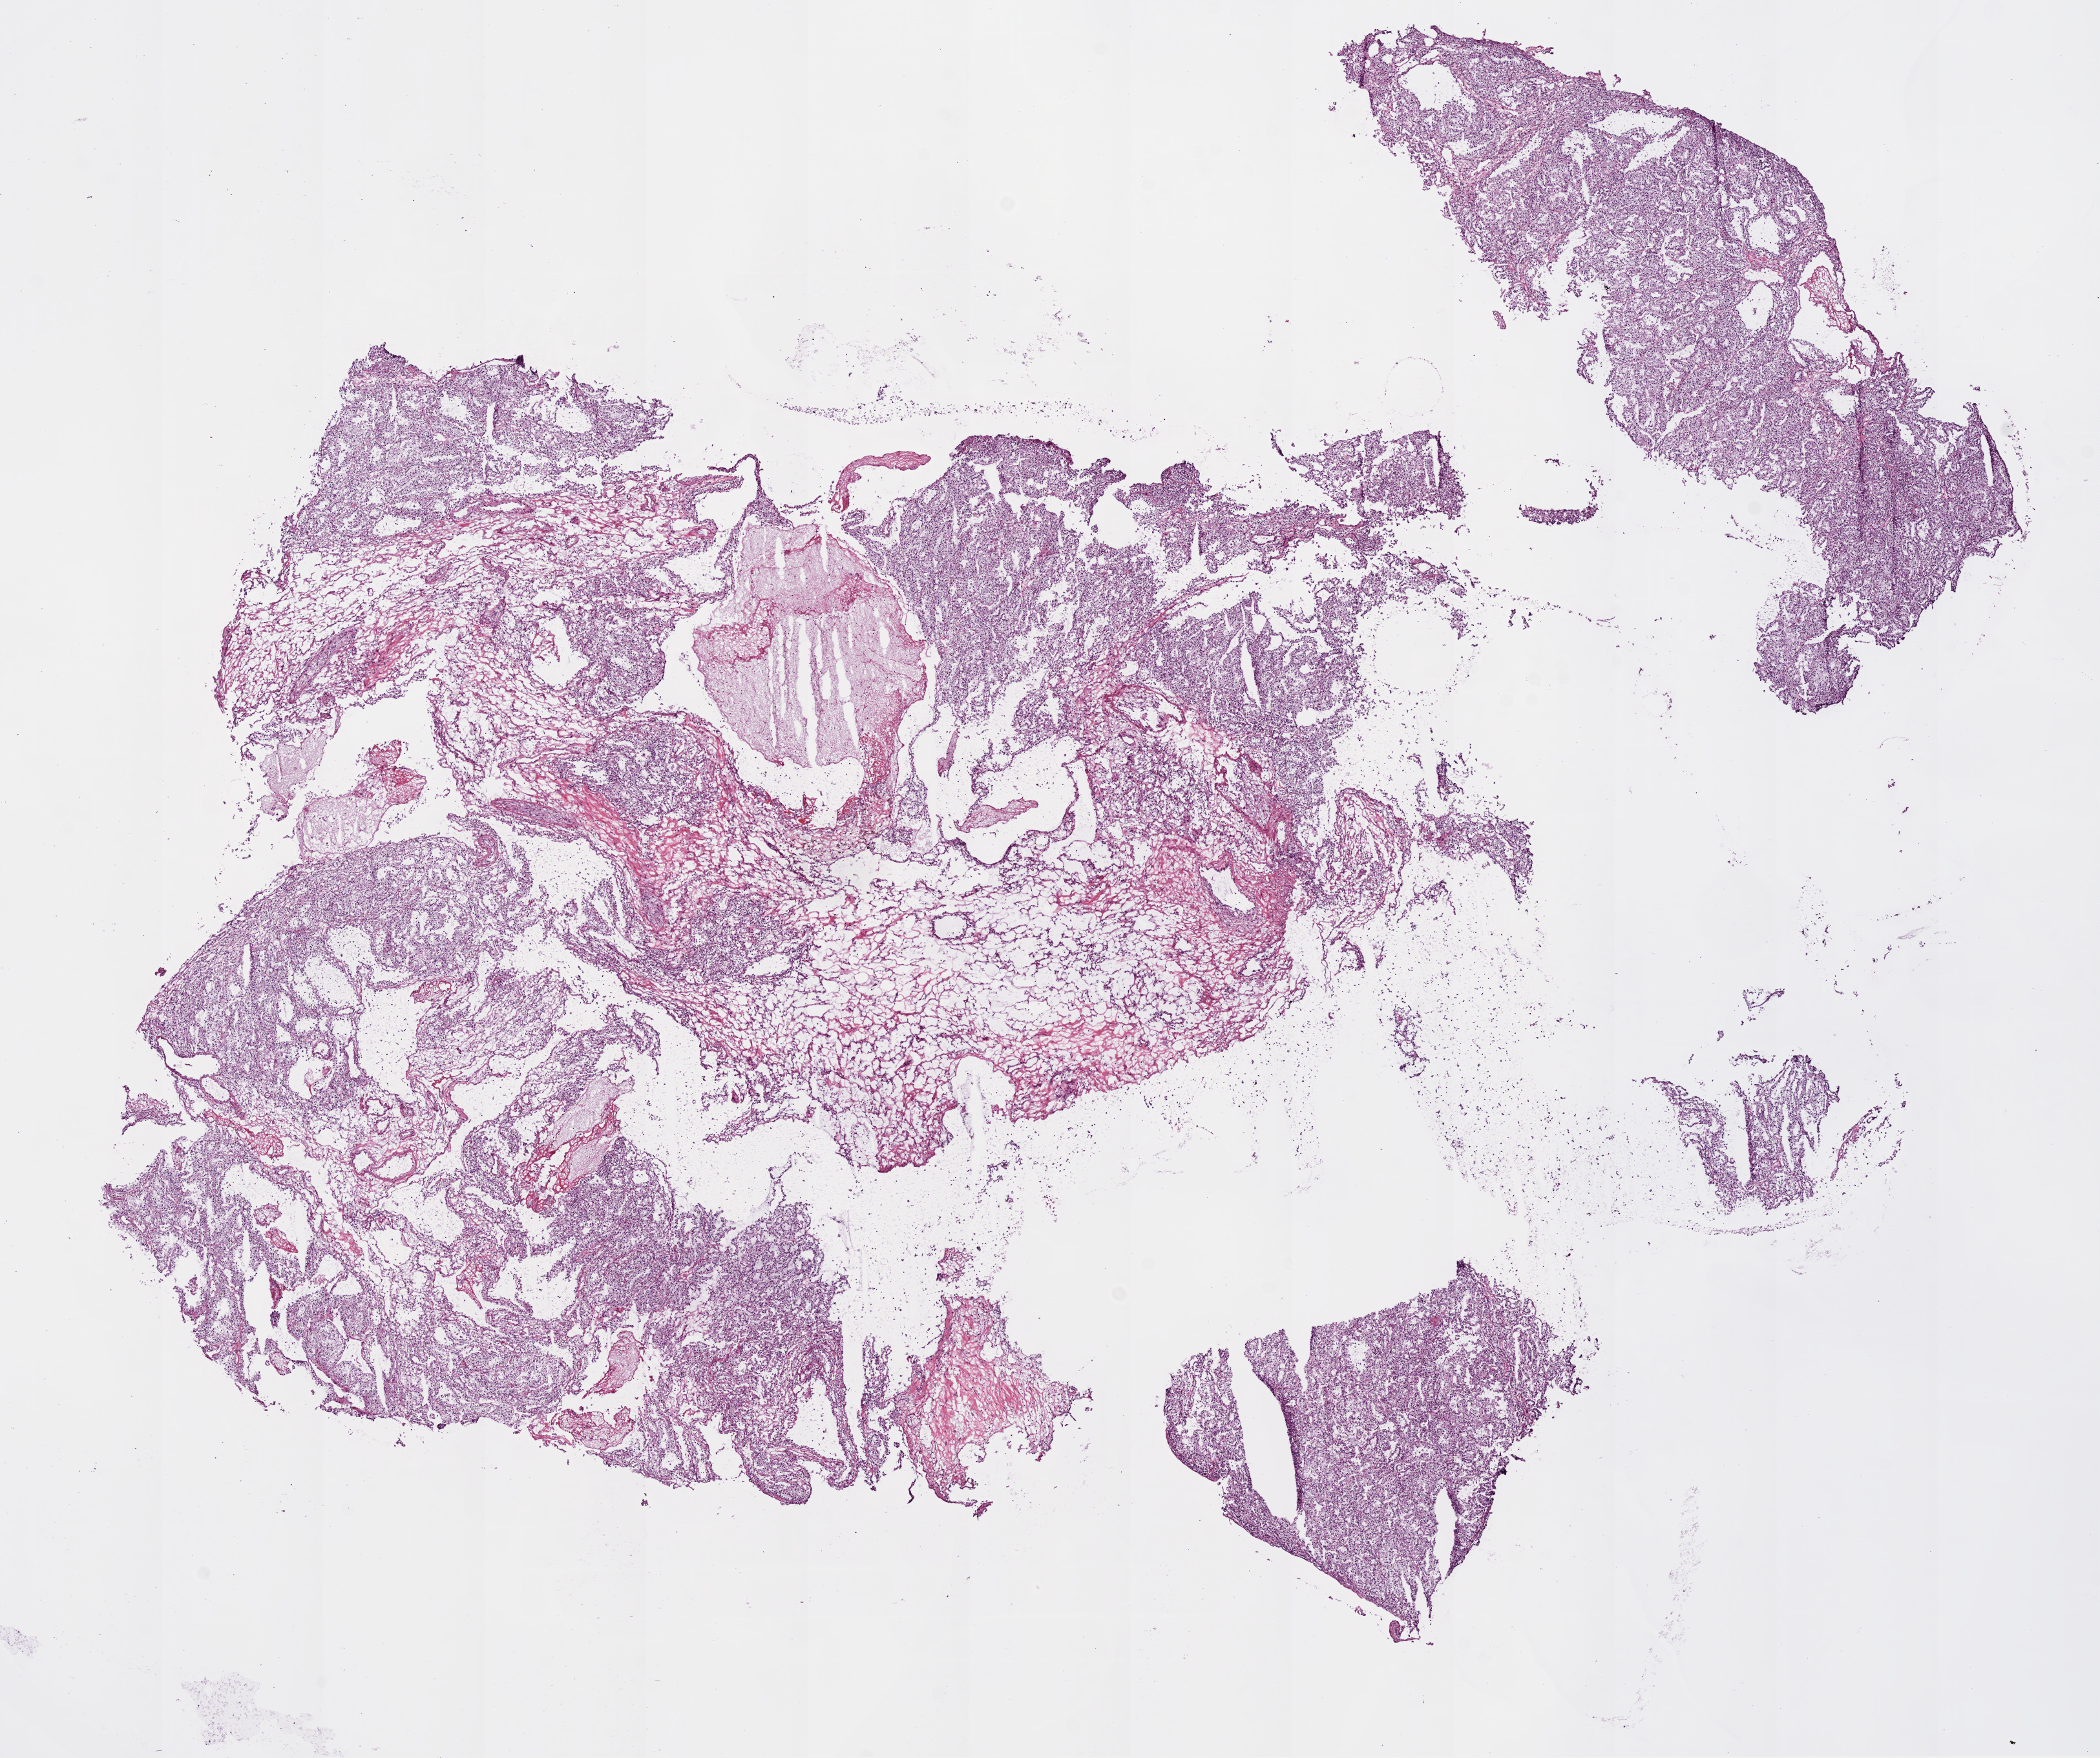
Whole-slide histology image, Hematoxylin and eosin (H&E) stained — low-resolution overview of the scanned area, about 13.0 x 10.9 mm (from a 20x scan), frozen section from the bottom of the tissue portion, sample: primary tumour, kidney. Female patient; age at initial diagnosis 29 years. Histologic grade: G2 (moderately differentiated). Pathologist review of this section (percent, as recorded): tumour cells 80%, tumour nuclei 80%, normal cells 0%, stromal cells 20%, necrosis 0%.
Diagnosis: Clear cell adenocarcinoma, NOS. AJCC pathologic stage: I. Laterality: right.